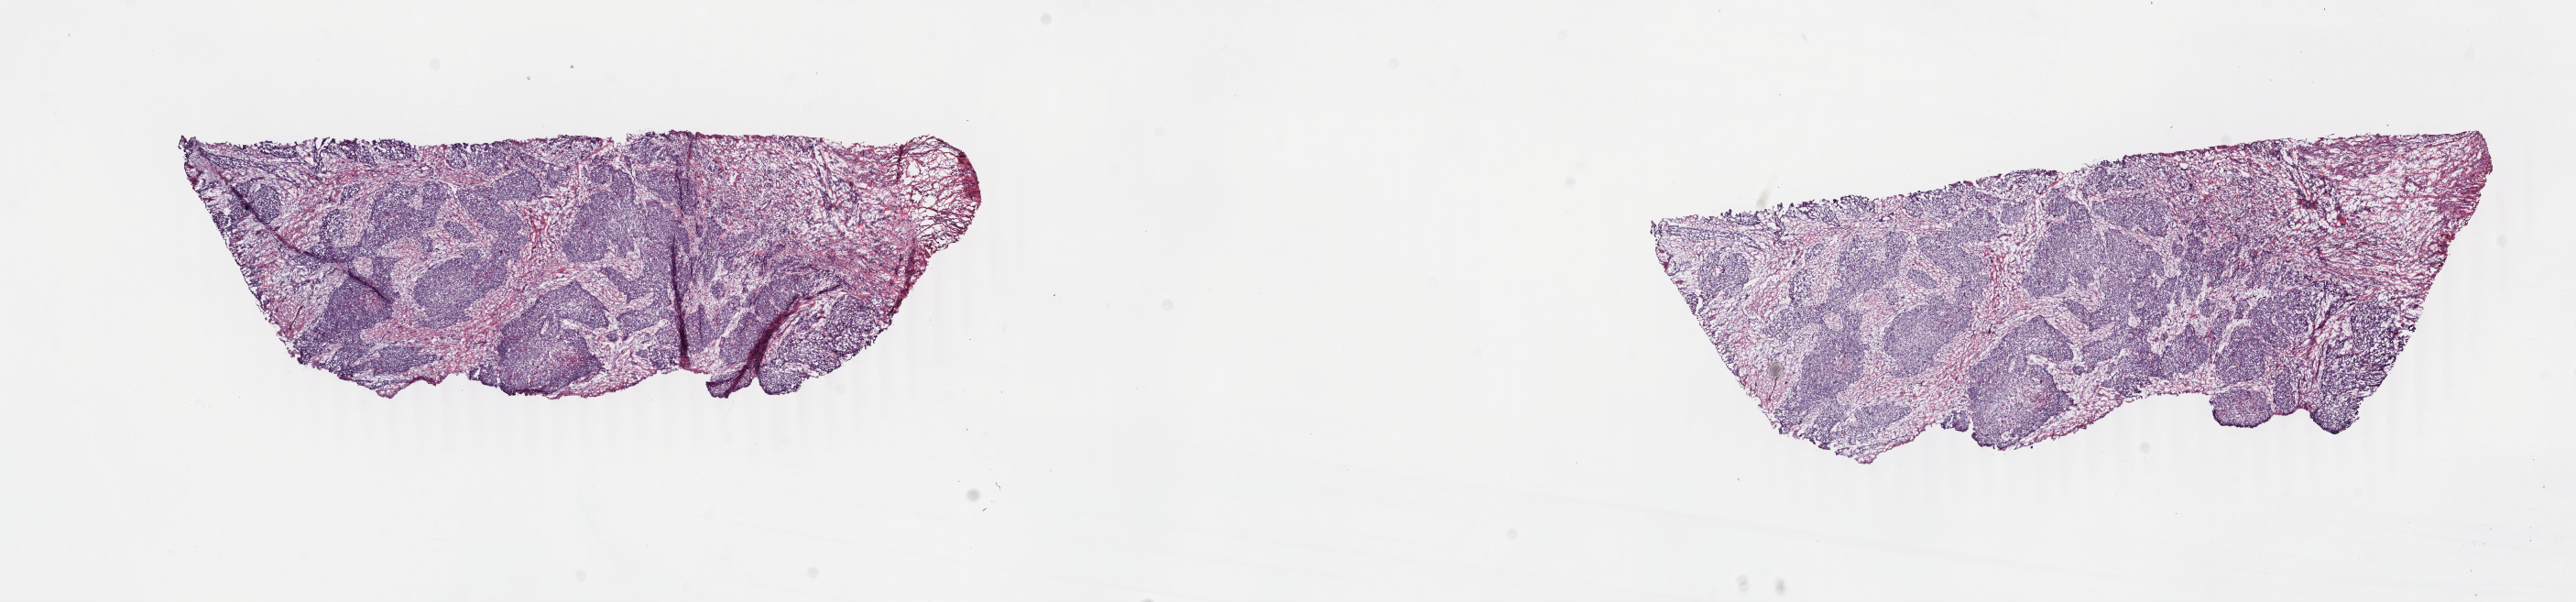
Whole-slide histology image, Hematoxylin and eosin (H&E) stained — low-resolution overview of the scanned area, about 22.4 x 5.2 mm (acquisition: 40x scan). Frozen section. Head and neck, primary tumour sample. Female patient; age at initial diagnosis 78 years. Histologic grade: G2 (moderately differentiated). Slide review estimates, as recorded: tumour cells 42%, tumour nuclei 80%, normal cells 0%, stromal cells 50%, necrosis 8%. Infiltration values recorded for this section: lymphocyte infiltration 6%, monocyte infiltration 1%, neutrophil infiltration 1%.
* AJCC pathologic stage: III
* laterality: left
* TNM: T3 N0 M0
* diagnosis: Squamous cell carcinoma, NOS (cheek mucosa)